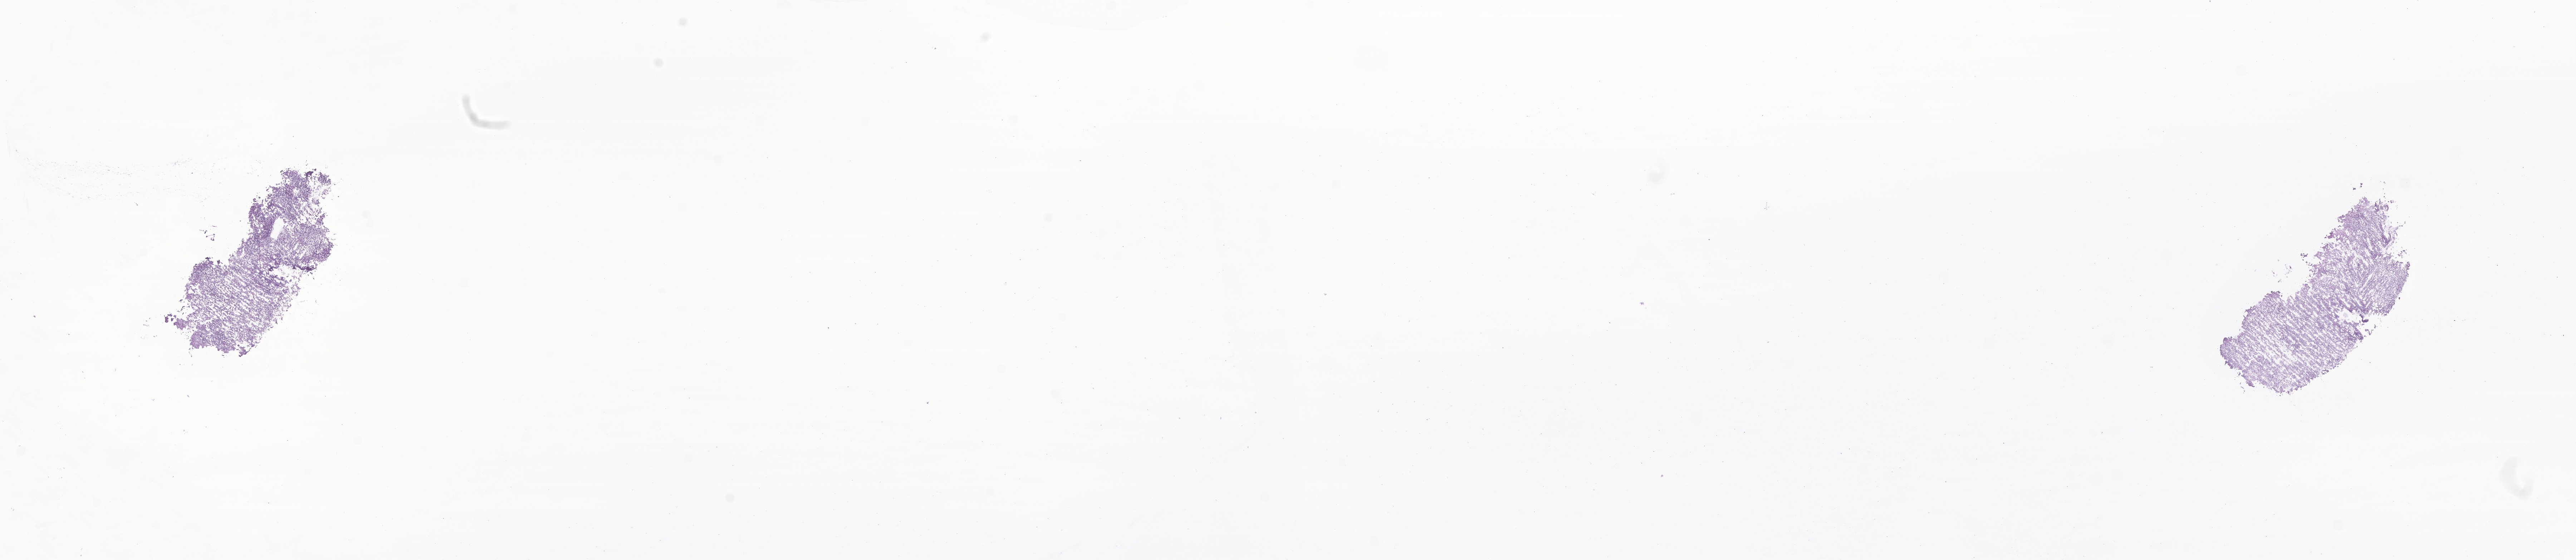
H&E whole-slide image of tumor tissue from the parietal lobe, whole scanned area (about 30.4 x 6.6 mm) shown as a low-resolution overview, frozen section. Patient: female, age 202 months.
* diagnosis (ICD-O-3 morphology term): Neoplasm, malignant